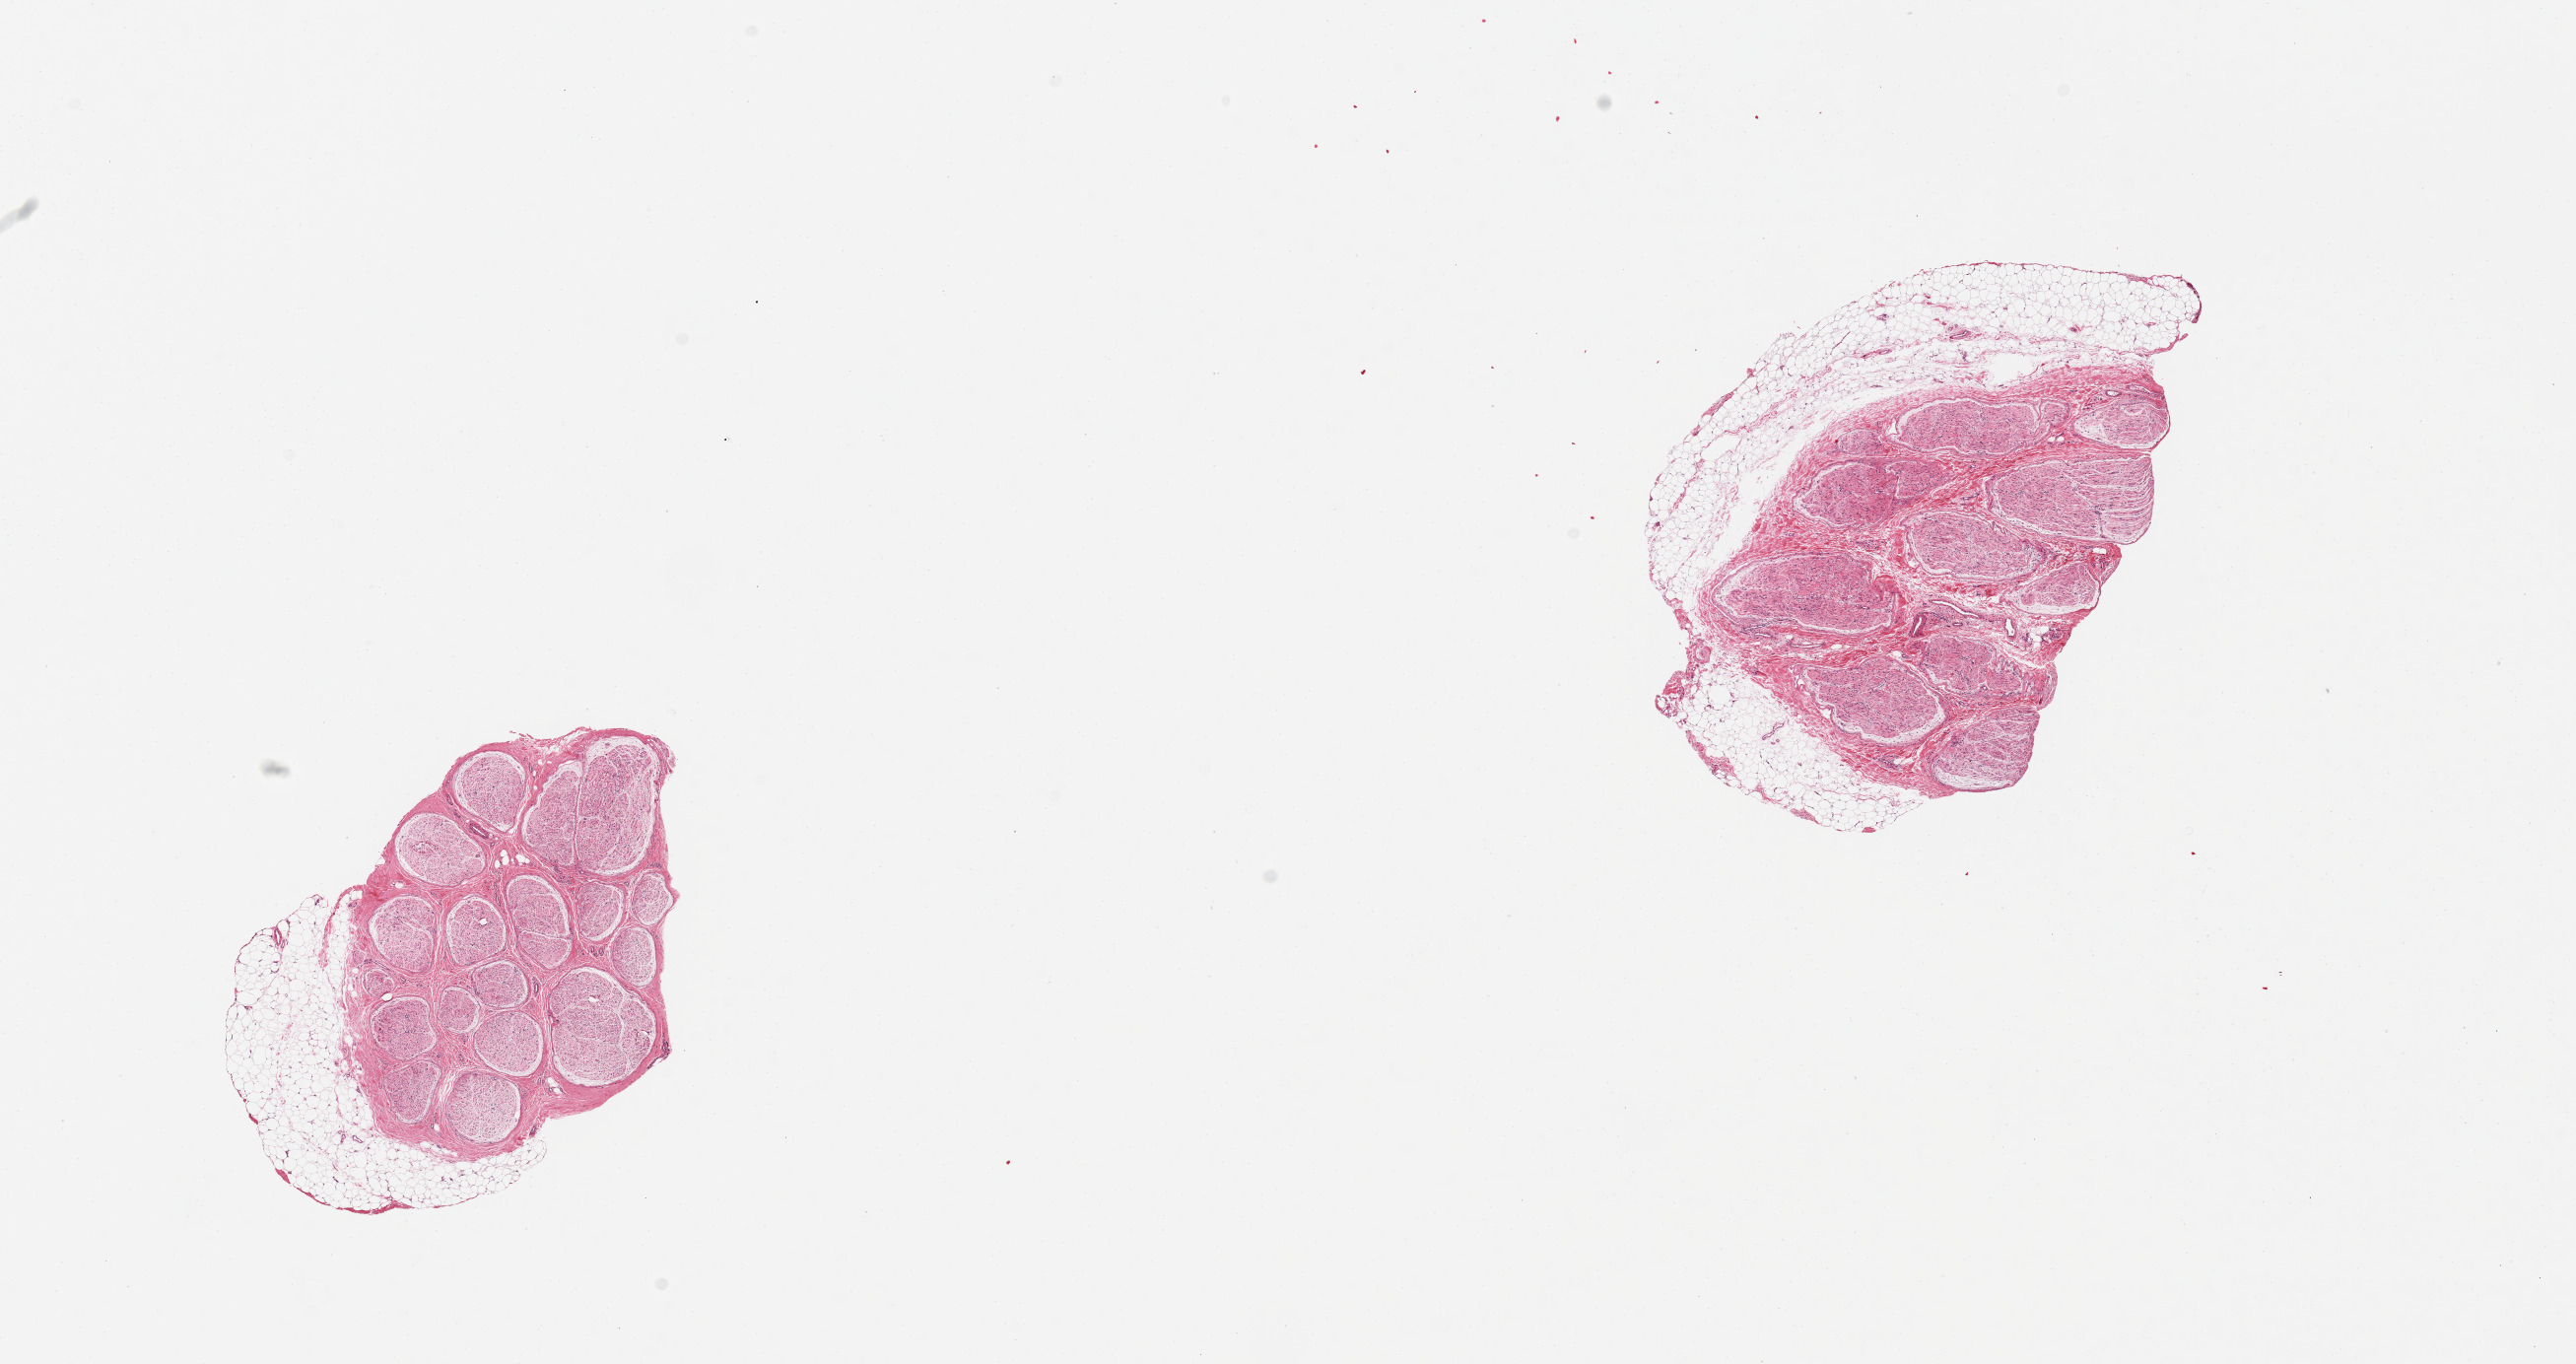
Haematoxylin and eosin whole-slide image, a low-resolution overview of the entire scanned area, about 20.7 x 10.9 mm. PAXgene-fixed paraffin-embedded (PFPE) section. Sampled site (target tissue): tibial nerve. Tissue donor sample. Donor: female.
Reviewer comment on this tissue sample: 2 pieces, incomplete rim of fat up to ~1mm.